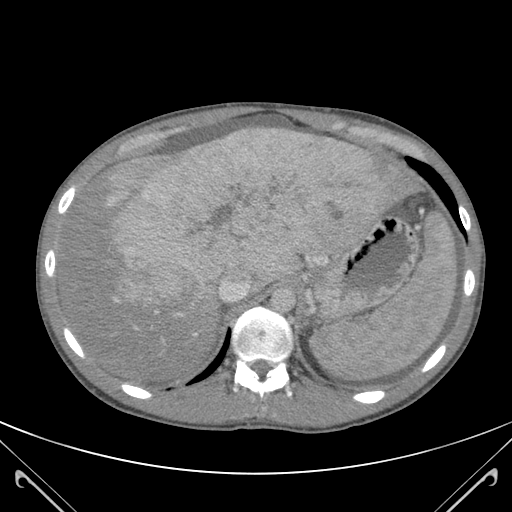
Contrast-enhanced abdominal CT (liver protocol), one axial slice. Position 90 of 118 along the scan axis. 120 kVp. Soft-tissue window (W 400 / L 40 HU). 3 mm slice thickness. 512 × 512 image matrix, field of view 380 × 380 mm. From the clinical record (not read from this slice): diagnosis: hepatocellular carcinoma (patient treated with transarterial chemoembolisation; whether this scan precedes or follows treatment is not stated here); TNM stage (as recorded): Stage-IIIB; Child-Pugh class: A; tumour nodularity: uninodular.
Outlined on this slice (semi-automatic segmentation, software-assisted and operator-edited):
- abdominal aorta: box from (x=273, y=287) to (x=297, y=311) px
- liver parenchyma outside the tumour (the mass and vessels are separate outlines, so this box may not span the whole liver): (x=61, y=126)–(x=422, y=378)
- mass: (x=98, y=127)–(x=416, y=322)
- liver vessels: (x=114, y=281)–(x=250, y=336)